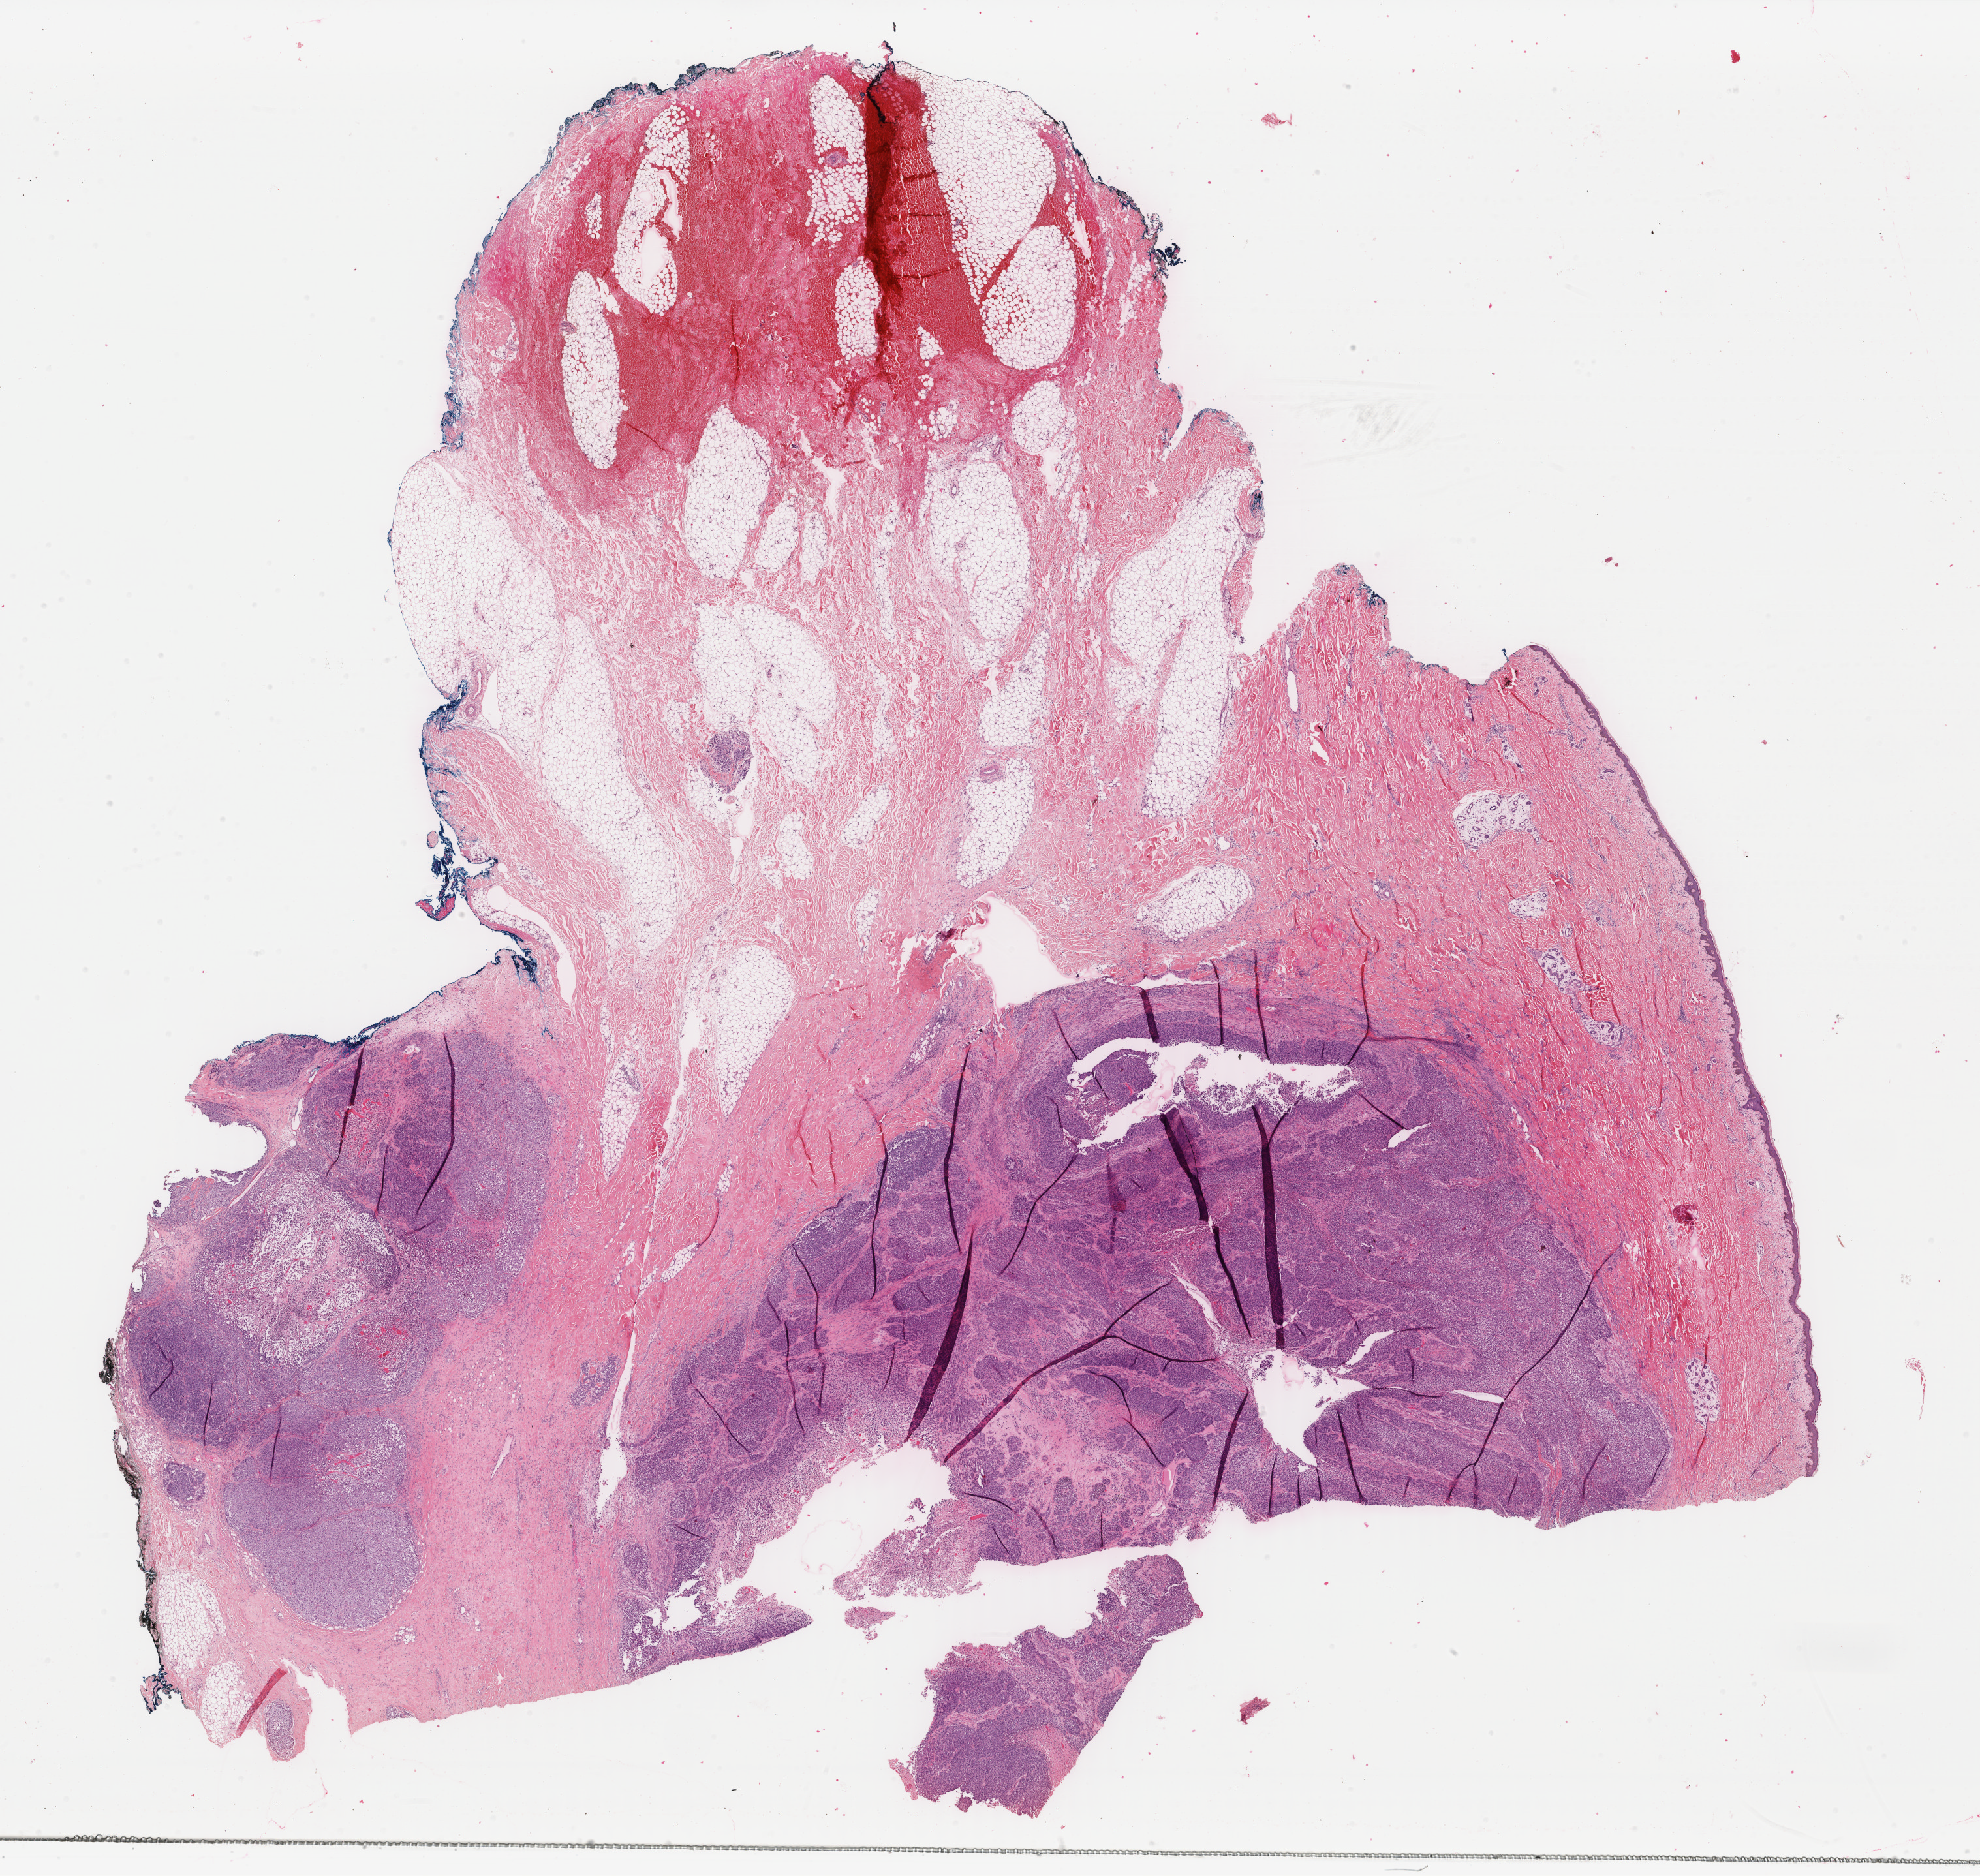
Whole-slide histology image, Hematoxylin and eosin (H&E) stained — a low-resolution overview of the entire scanned area, about 24.1 x 22.8 mm. FFPE section. Metastatic tumour sample. Male patient; age at initial diagnosis 69 years.
This section: metastatic tumour tissue. Patient diagnosis: Malignant melanoma, NOS.